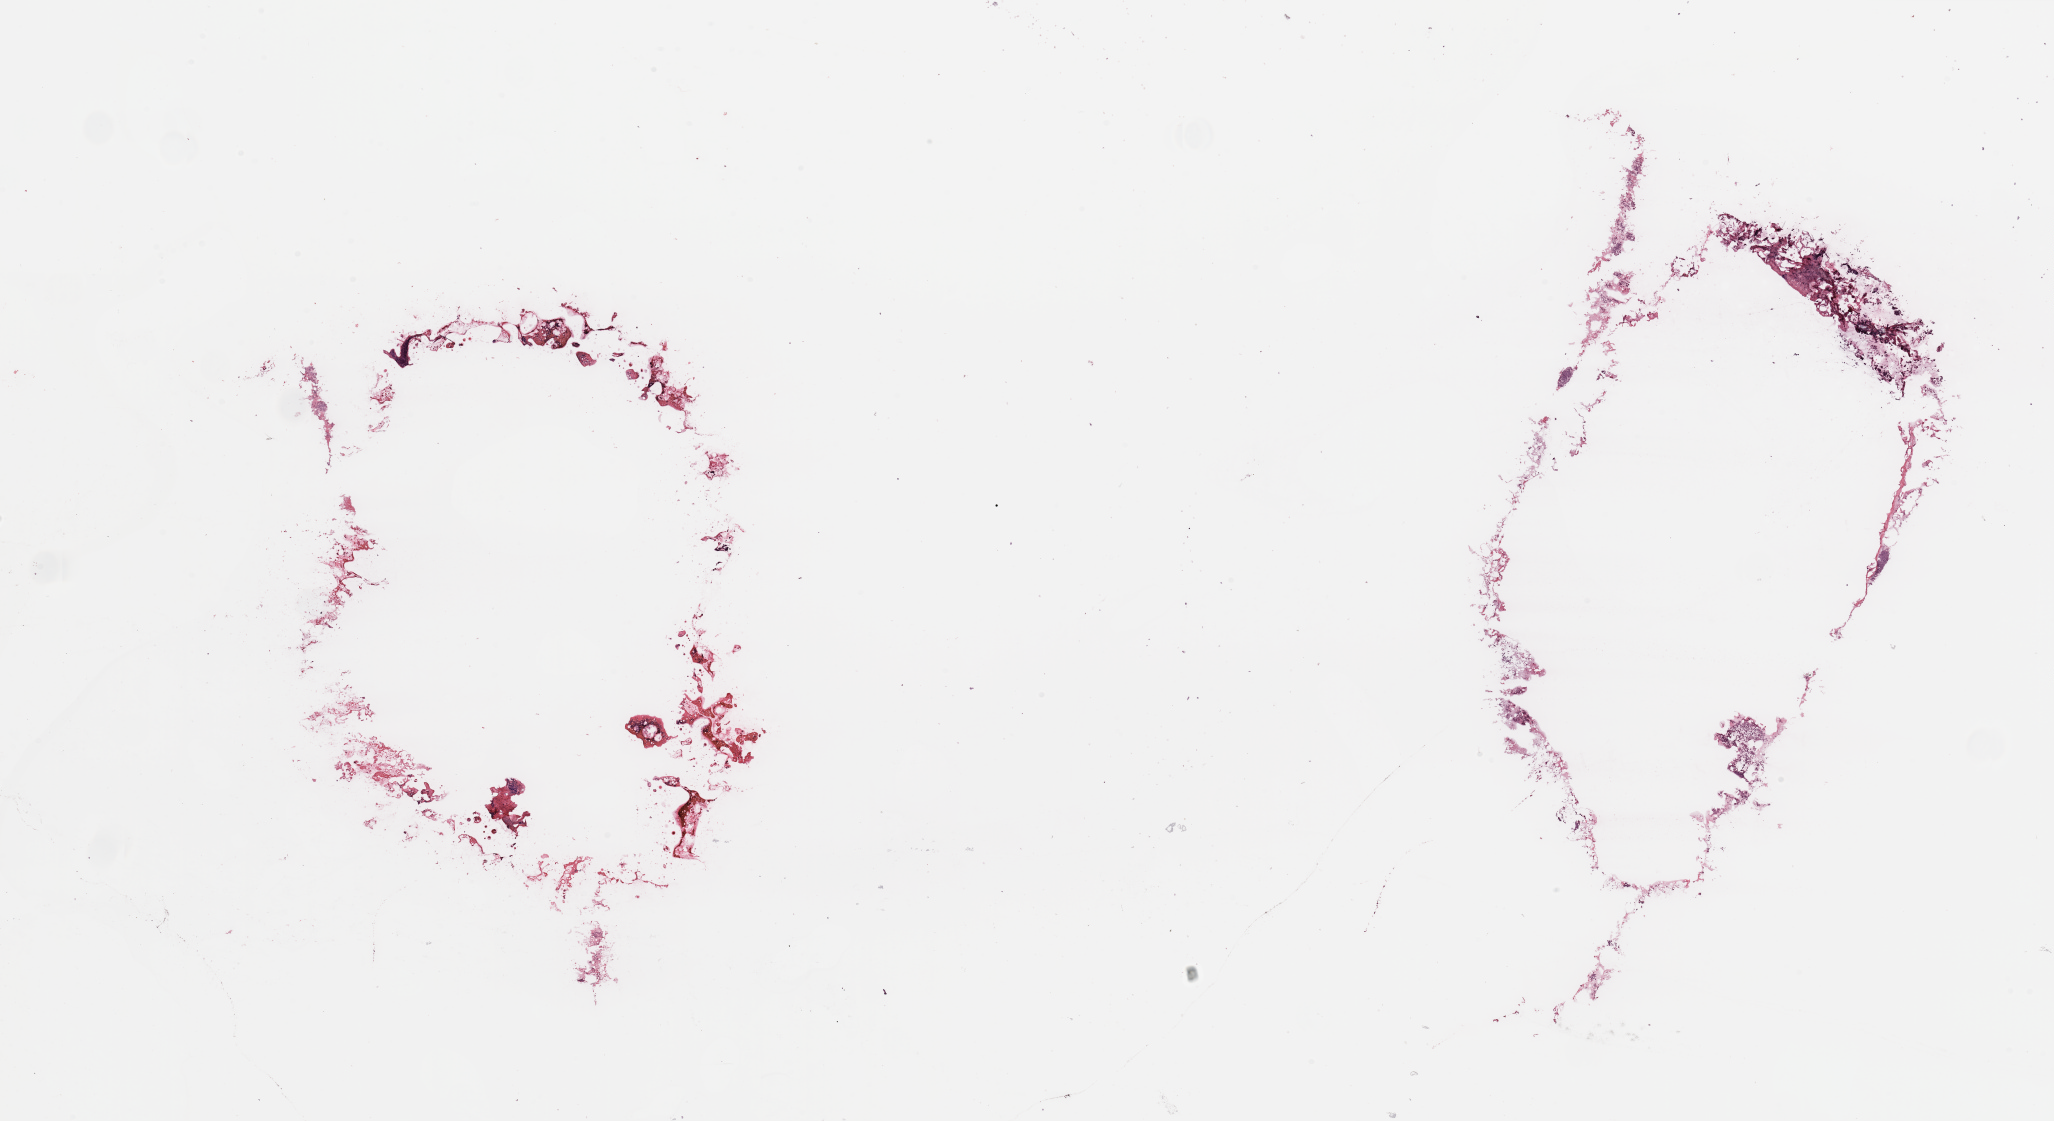
Whole-slide histology image, H&E, whole scanned area (about 32.5 x 17.7 mm) shown as a low-resolution overview, breast, tissue type not recorded.
• patient diagnosis (cohort enrolment): breast cancer (breast)